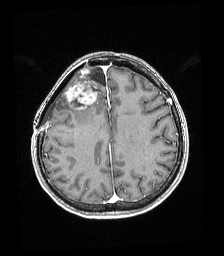
Brain MRI from a brain-tumour surgery series, one axial slice; slice 66 of 192 in the series (ordered by position); T1-weighted post-contrast; 224 × 256 image matrix. Case-level facts recorded for this patient, not image findings: histopathology: Astrocytoma; WHO grade: 4; IDH mutation: yes; tumour location: Right superficial frontal.
Annotated regions visible in this slice (outlined manually by an expert reader):
- tumour: bounding box (x1, y1, x2, y2) in pixels: (66, 66, 98, 110)